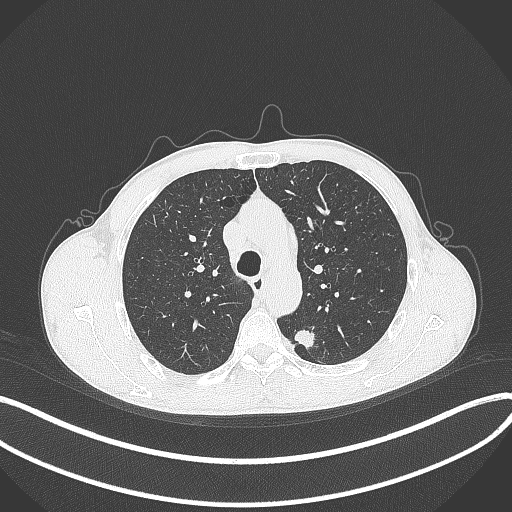
Chest CT, one axial slice. Slice 283 of 429 in the series (ordered by position). Reconstruction kernel B70f. 120 kVp. Lung window (W 1500 / L -600 HU). 512 × 512 image matrix, field of view 400 × 400 mm. Patient: male, 51 years. From the clinical record (not read from this slice): clinical TNM (as recorded): T2a N1 M1.
Outlined on this slice (rectangle marked by the reading radiologist):
- lung tumour (recorded histology: adenocarcinoma): bounding box <294,326,318,352> (left, top, right, bottom; pixels)